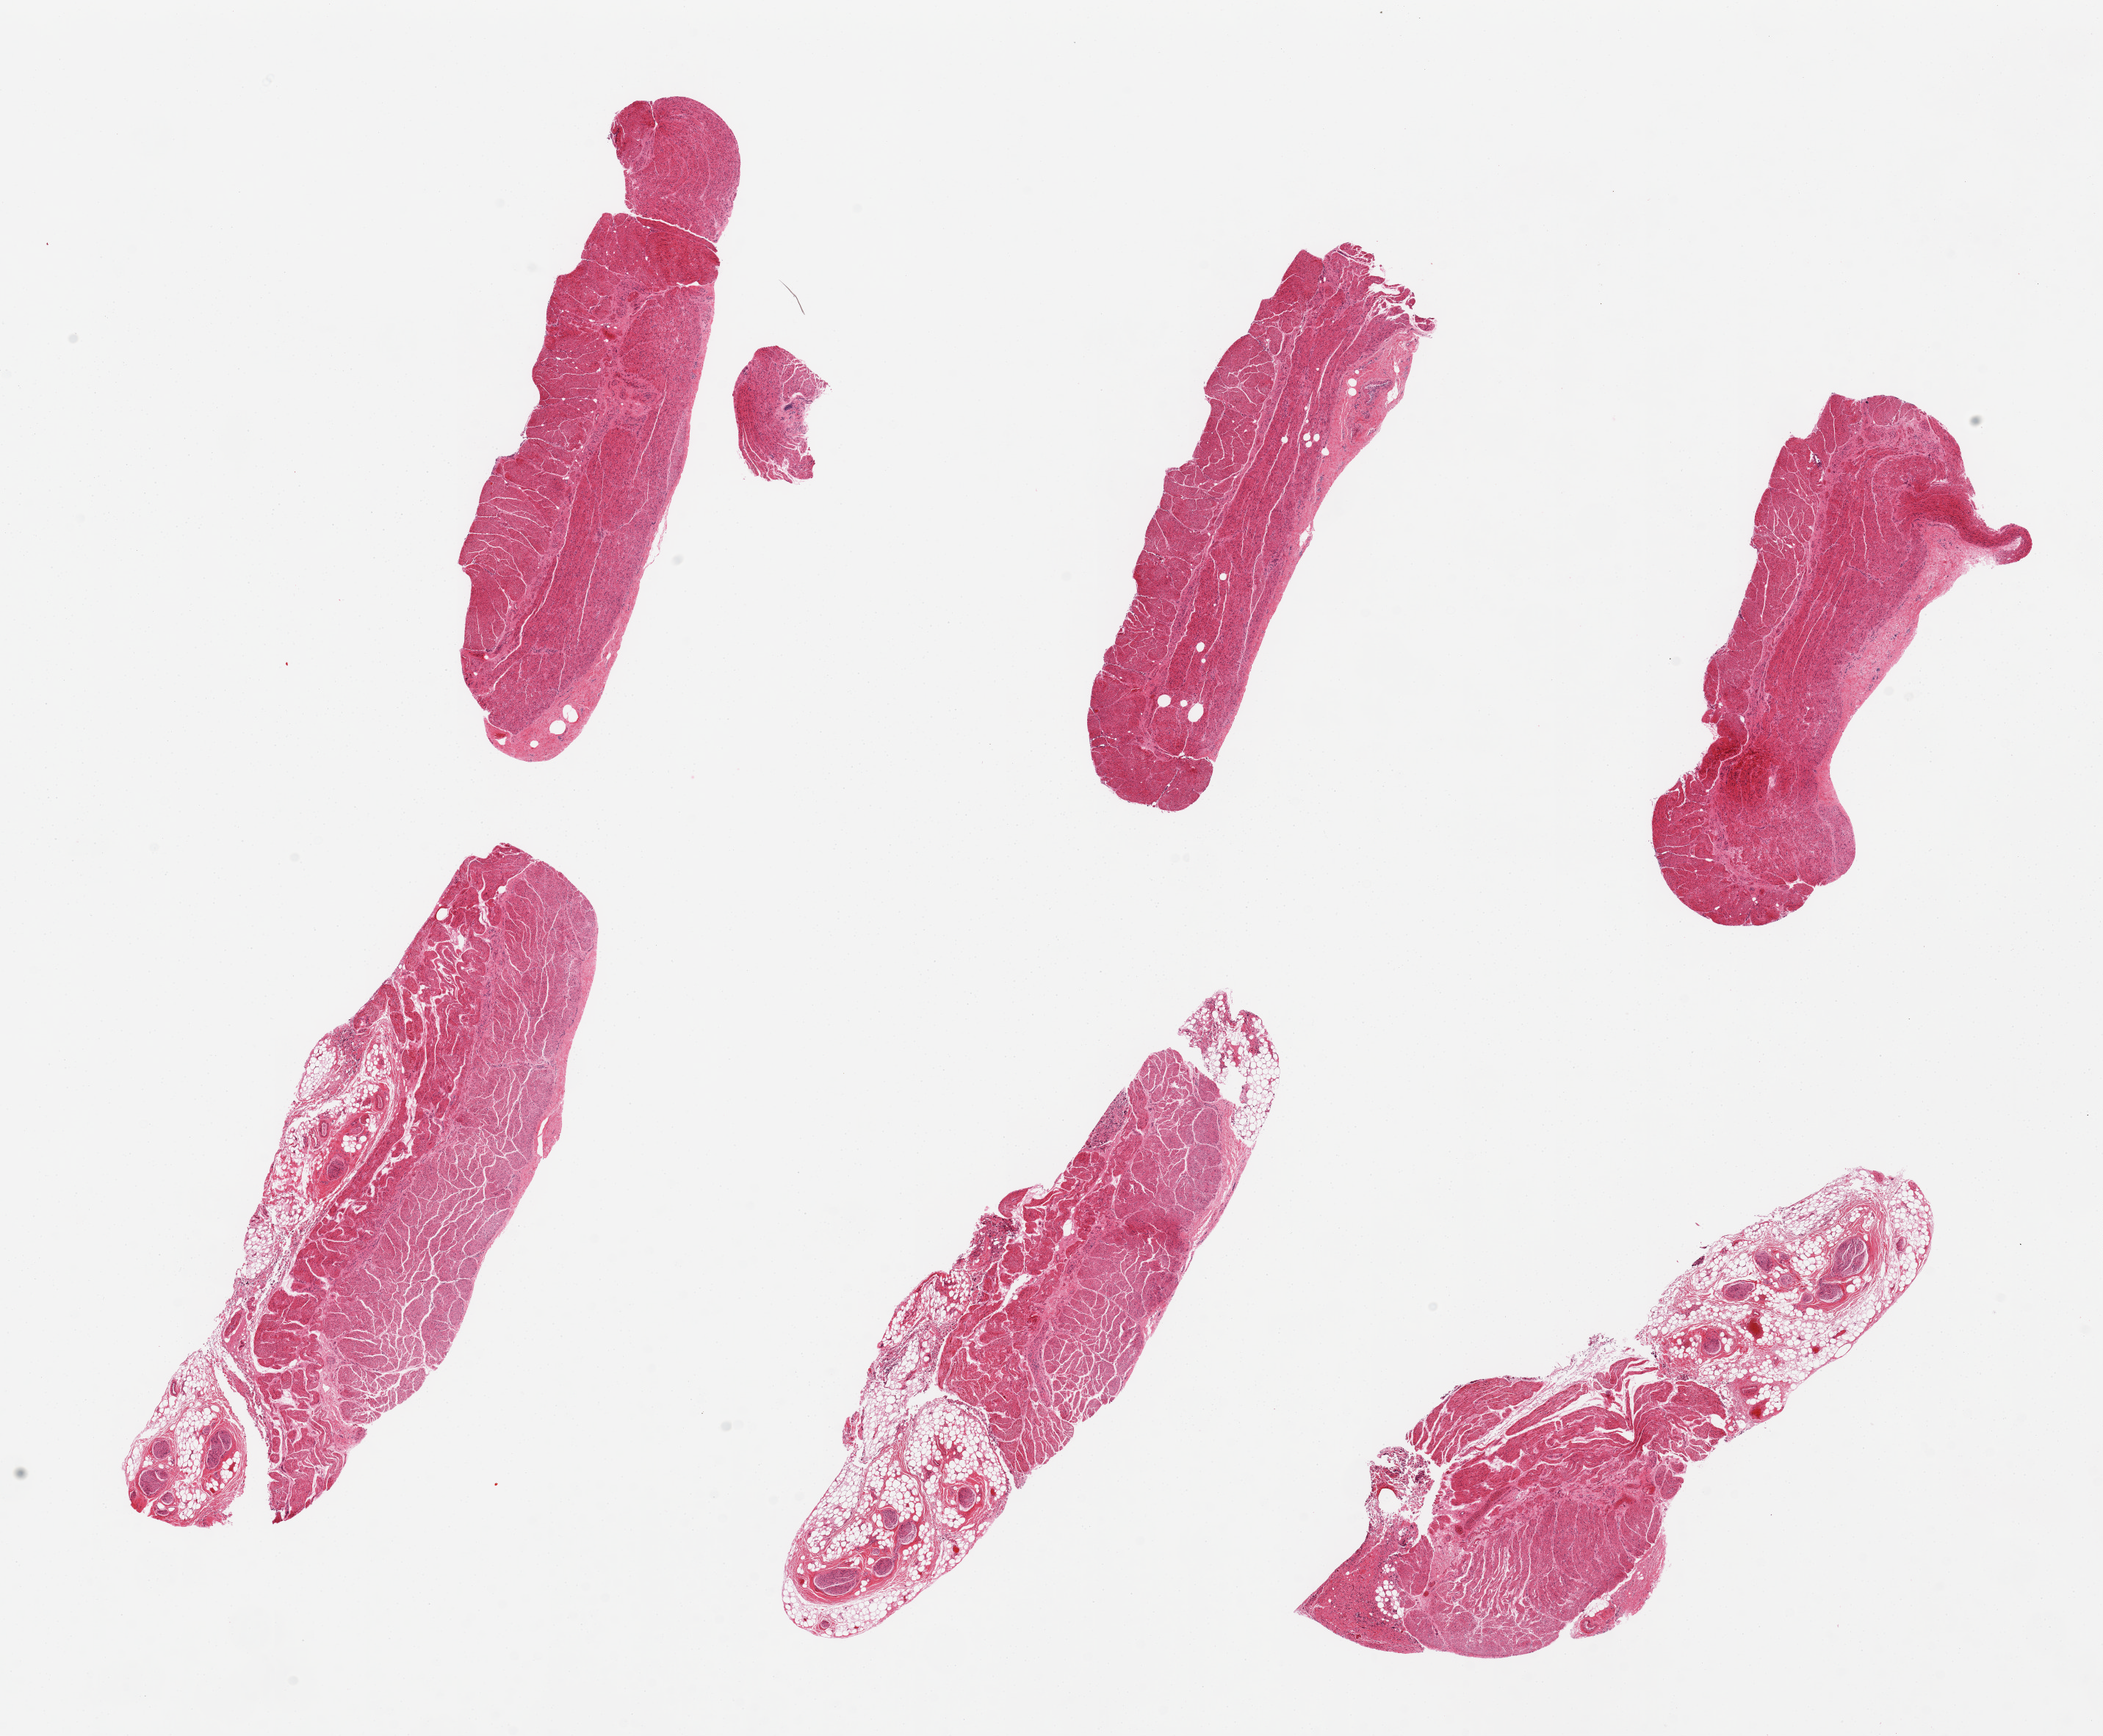
Digitized H&E-stained section — shown as a low-resolution overview of the whole scanned area (about 22.6 x 18.7 mm, from a 20x scan). PAXgene-fixed, paraffin-embedded tissue. Target tissue: esophageal muscle. Donor tissue sample.
Review note (as recorded): 6 pieces: 3 well trimmed muscle, 3 with 20 - 50% adventitial fat.